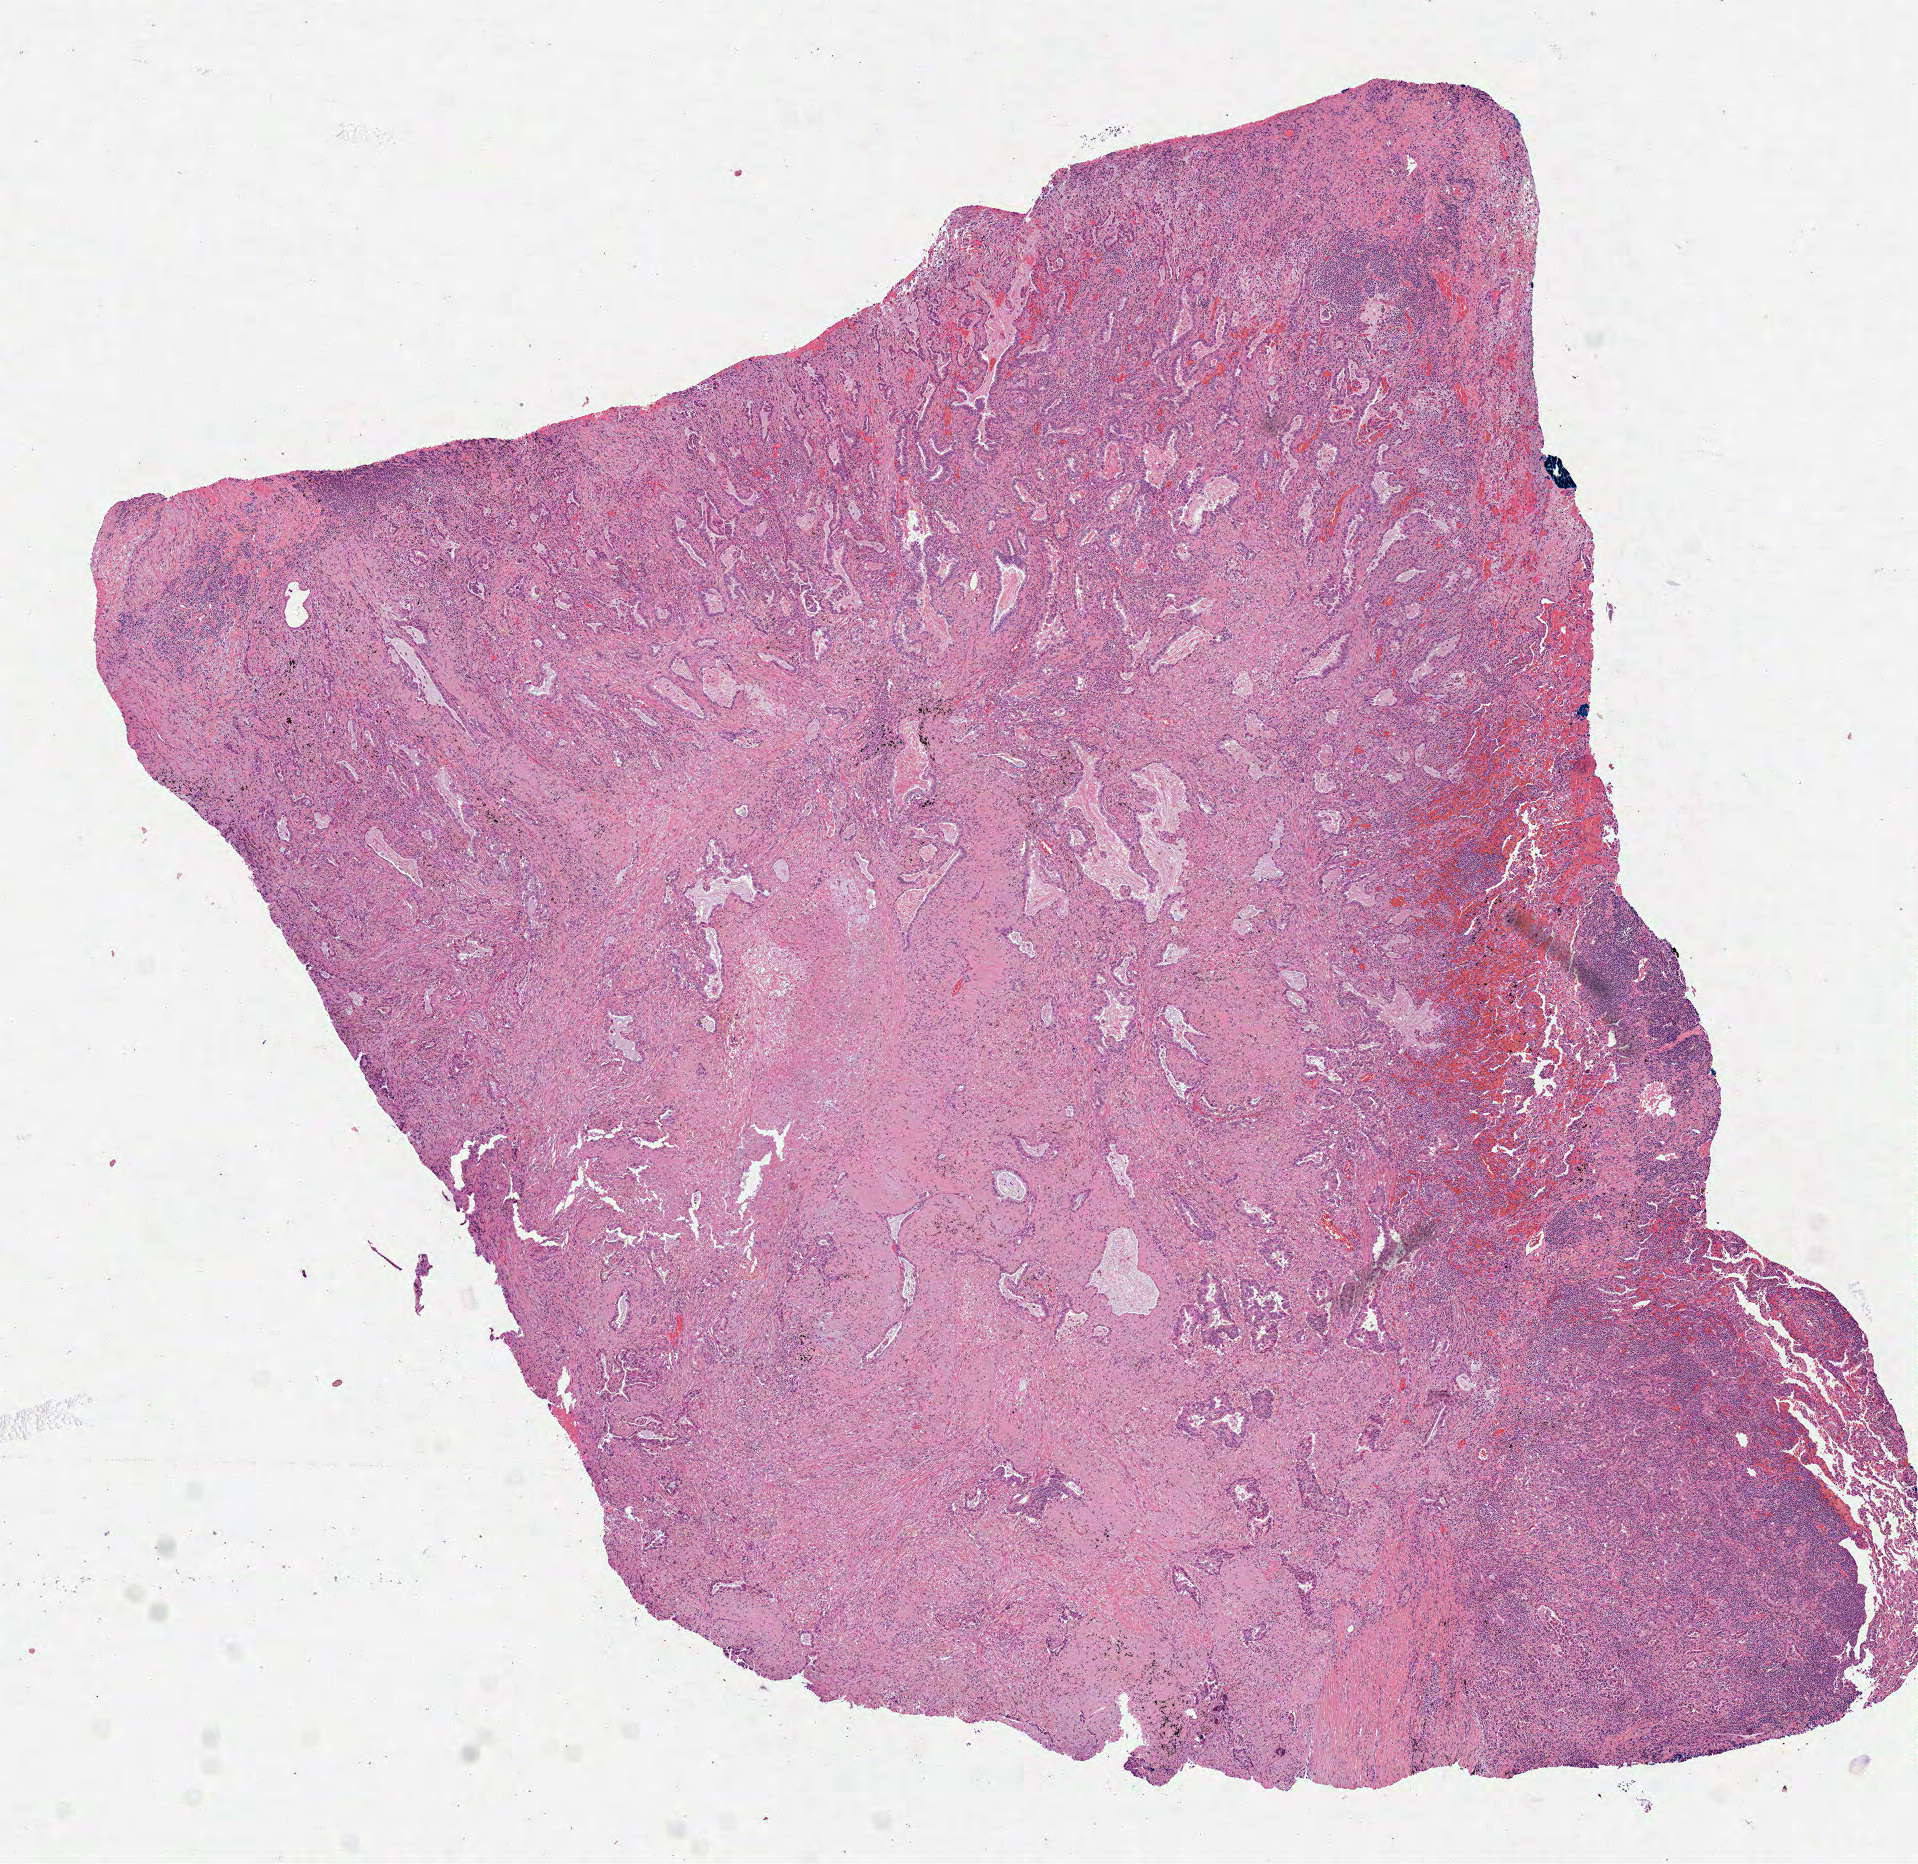
Whole-slide histology image, H&E — low-resolution overview of the scanned area, about 7.7 x 7.5 mm (slide scanned at 40x); FFPE section; sample: primary tumour, lung. Female, age 58 years at initial diagnosis.
Laterality: left. AJCC pathologic stage: IB. TNM: T2 N0 MX. Diagnosis: Adenocarcinoma, NOS (upper lobe, lung).